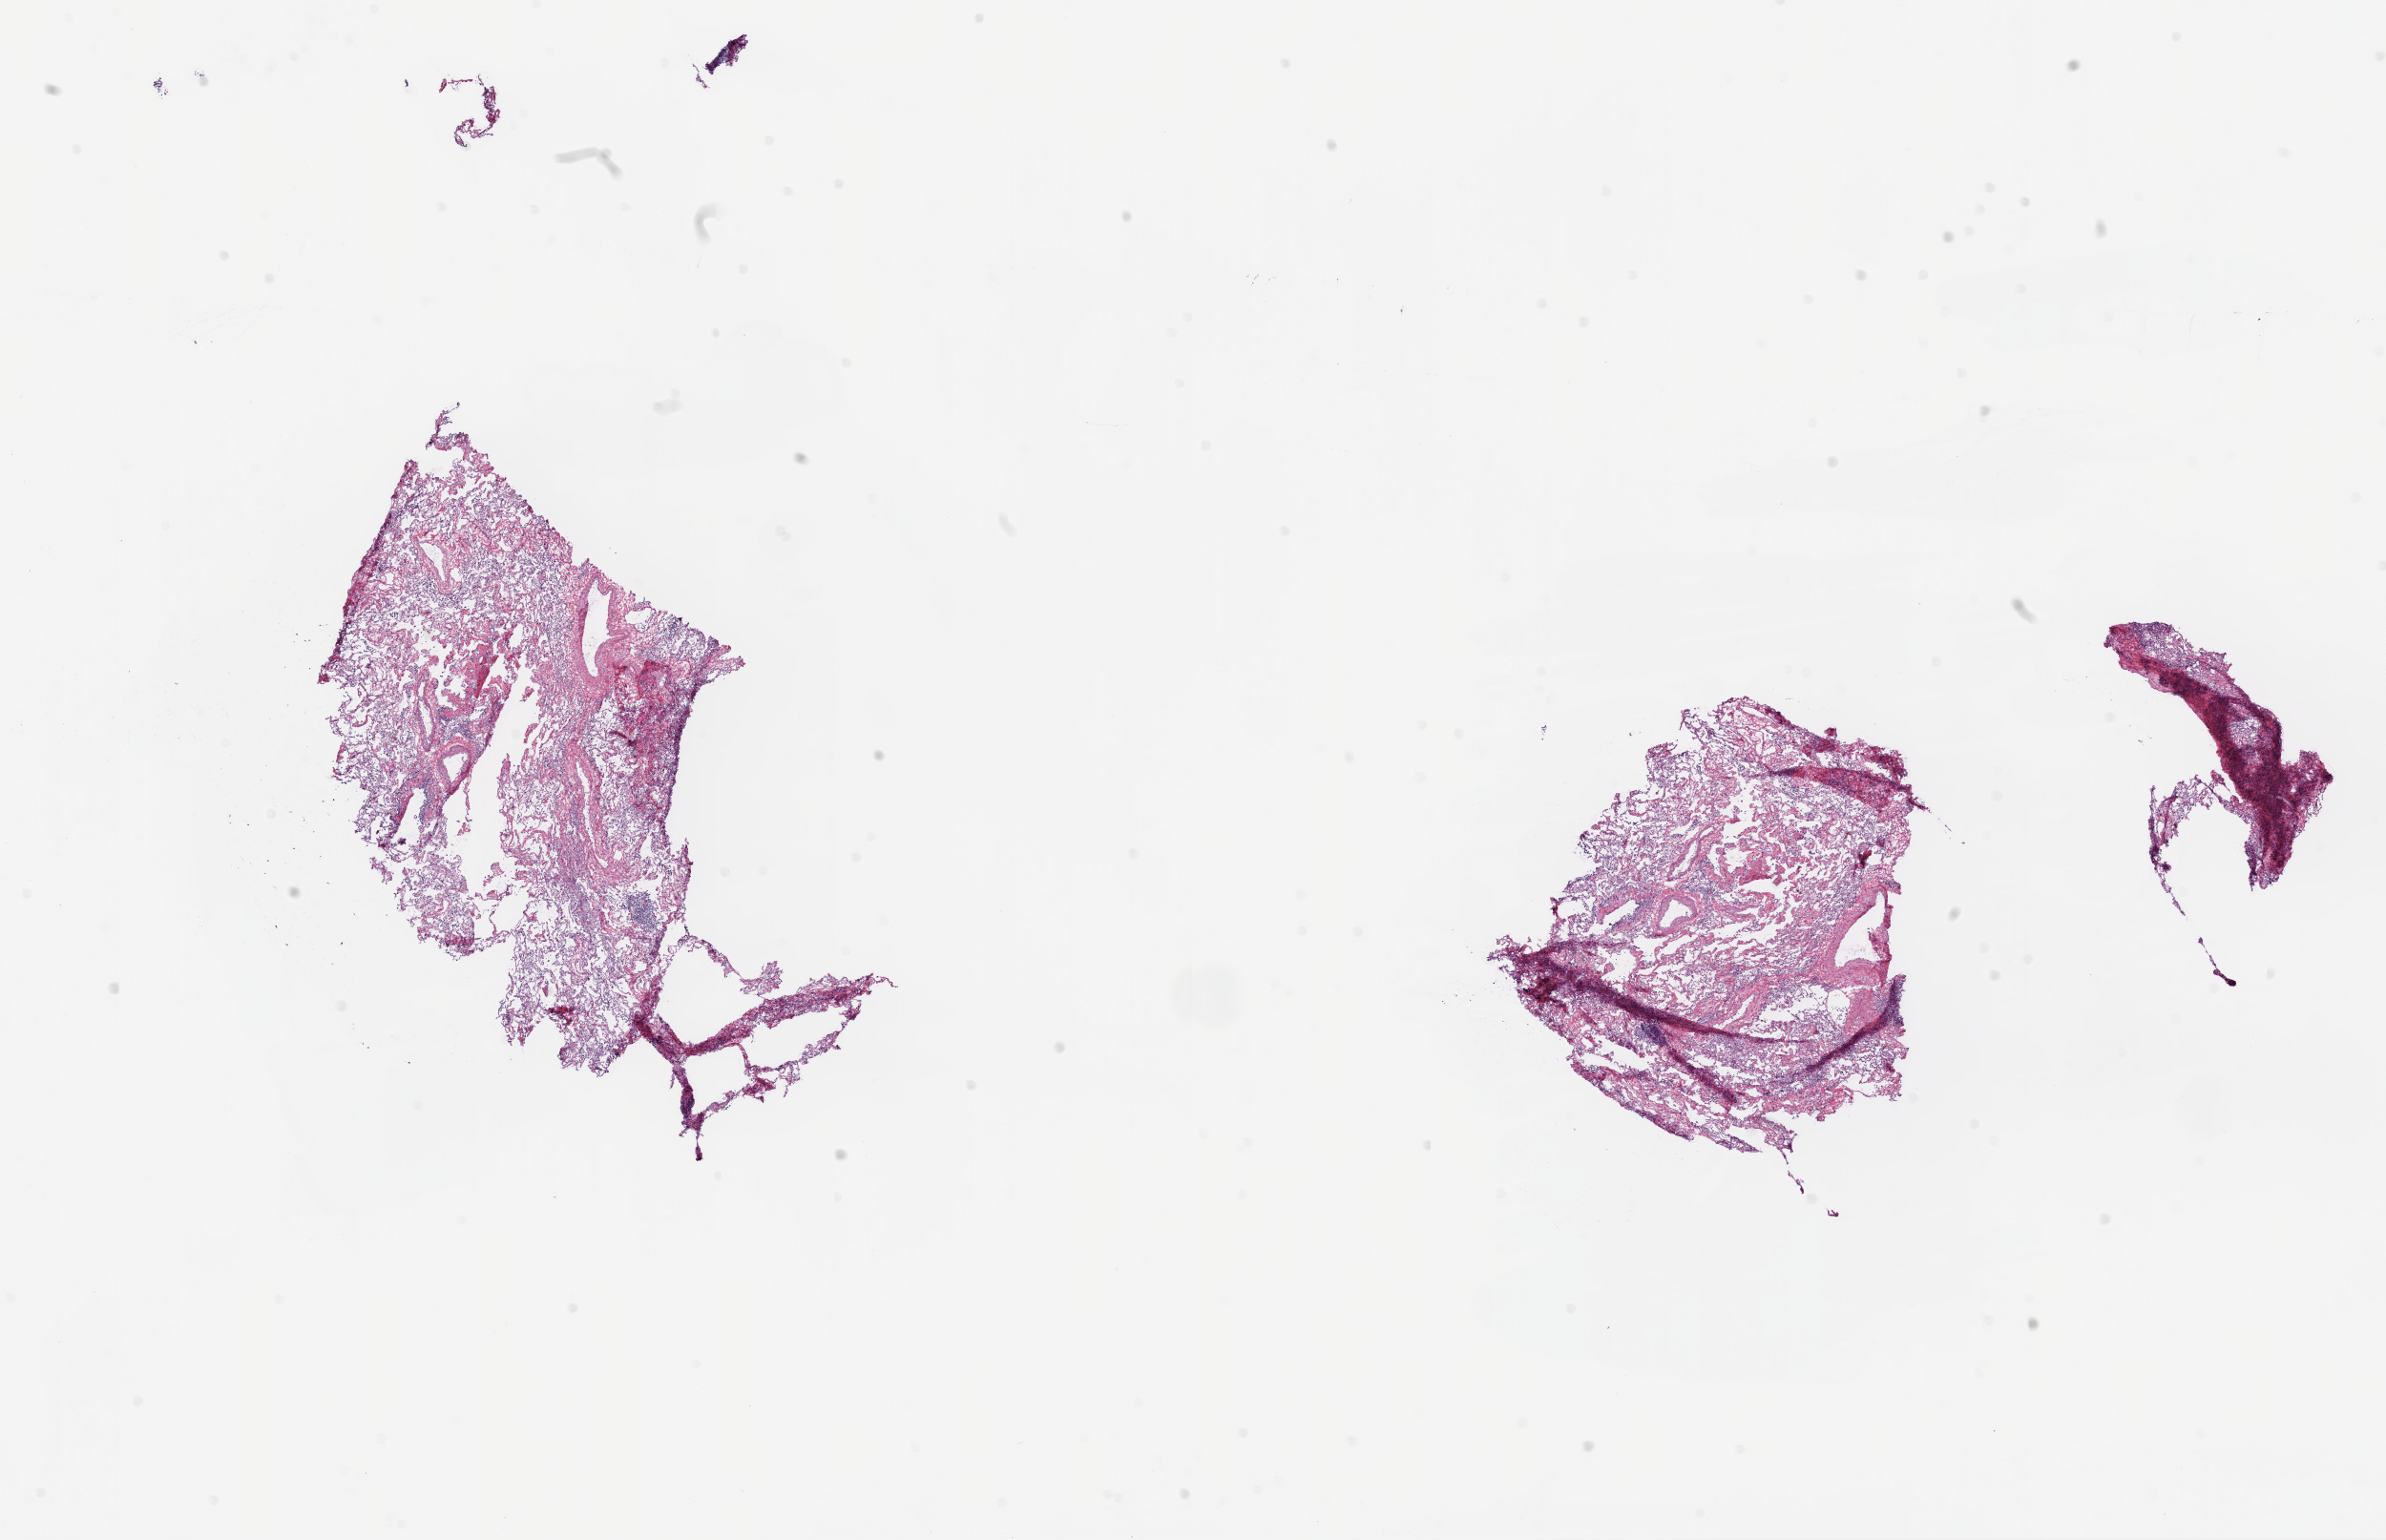
H&E-stained whole-slide image, low-resolution overview of the scanned area, about 20.1 x 13.0 mm. Frozen section from the top of the tissue portion. Sample: solid tissue normal (non-tumour tissue), lung. Patient: female, age at initial diagnosis 63 years.
This section: solid tissue normal (non-tumour) sample from the same patient. Patient diagnosis: Squamous cell carcinoma, NOS (upper lobe, lung).